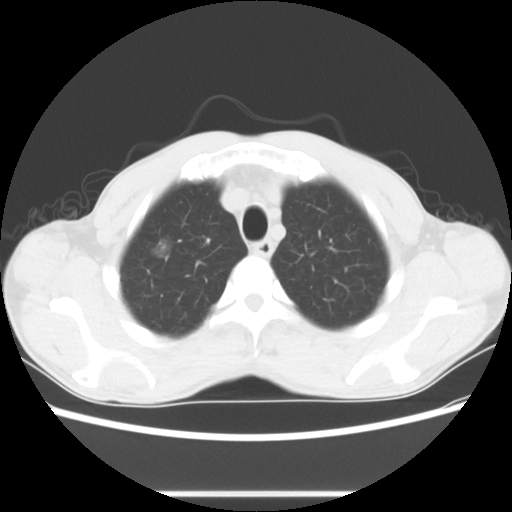
Chest CT, one axial slice; slice 63 of 76 in the series (ordered by position); reconstruction kernel STANDARD; lung window (W 1500 / L -600 HU); 5 mm slice thickness; 512 × 512 image matrix, field of view 357 × 357 mm. Patient: male, 54 years. From the clinical record (not read from this slice): clinical TNM (as recorded): T1a N0 M0.
Outlined on this slice (rectangle marked by the reading radiologist):
- lung tumour (recorded histology: adenocarcinoma): bounding box <151,231,181,266> (left, top, right, bottom; pixels)